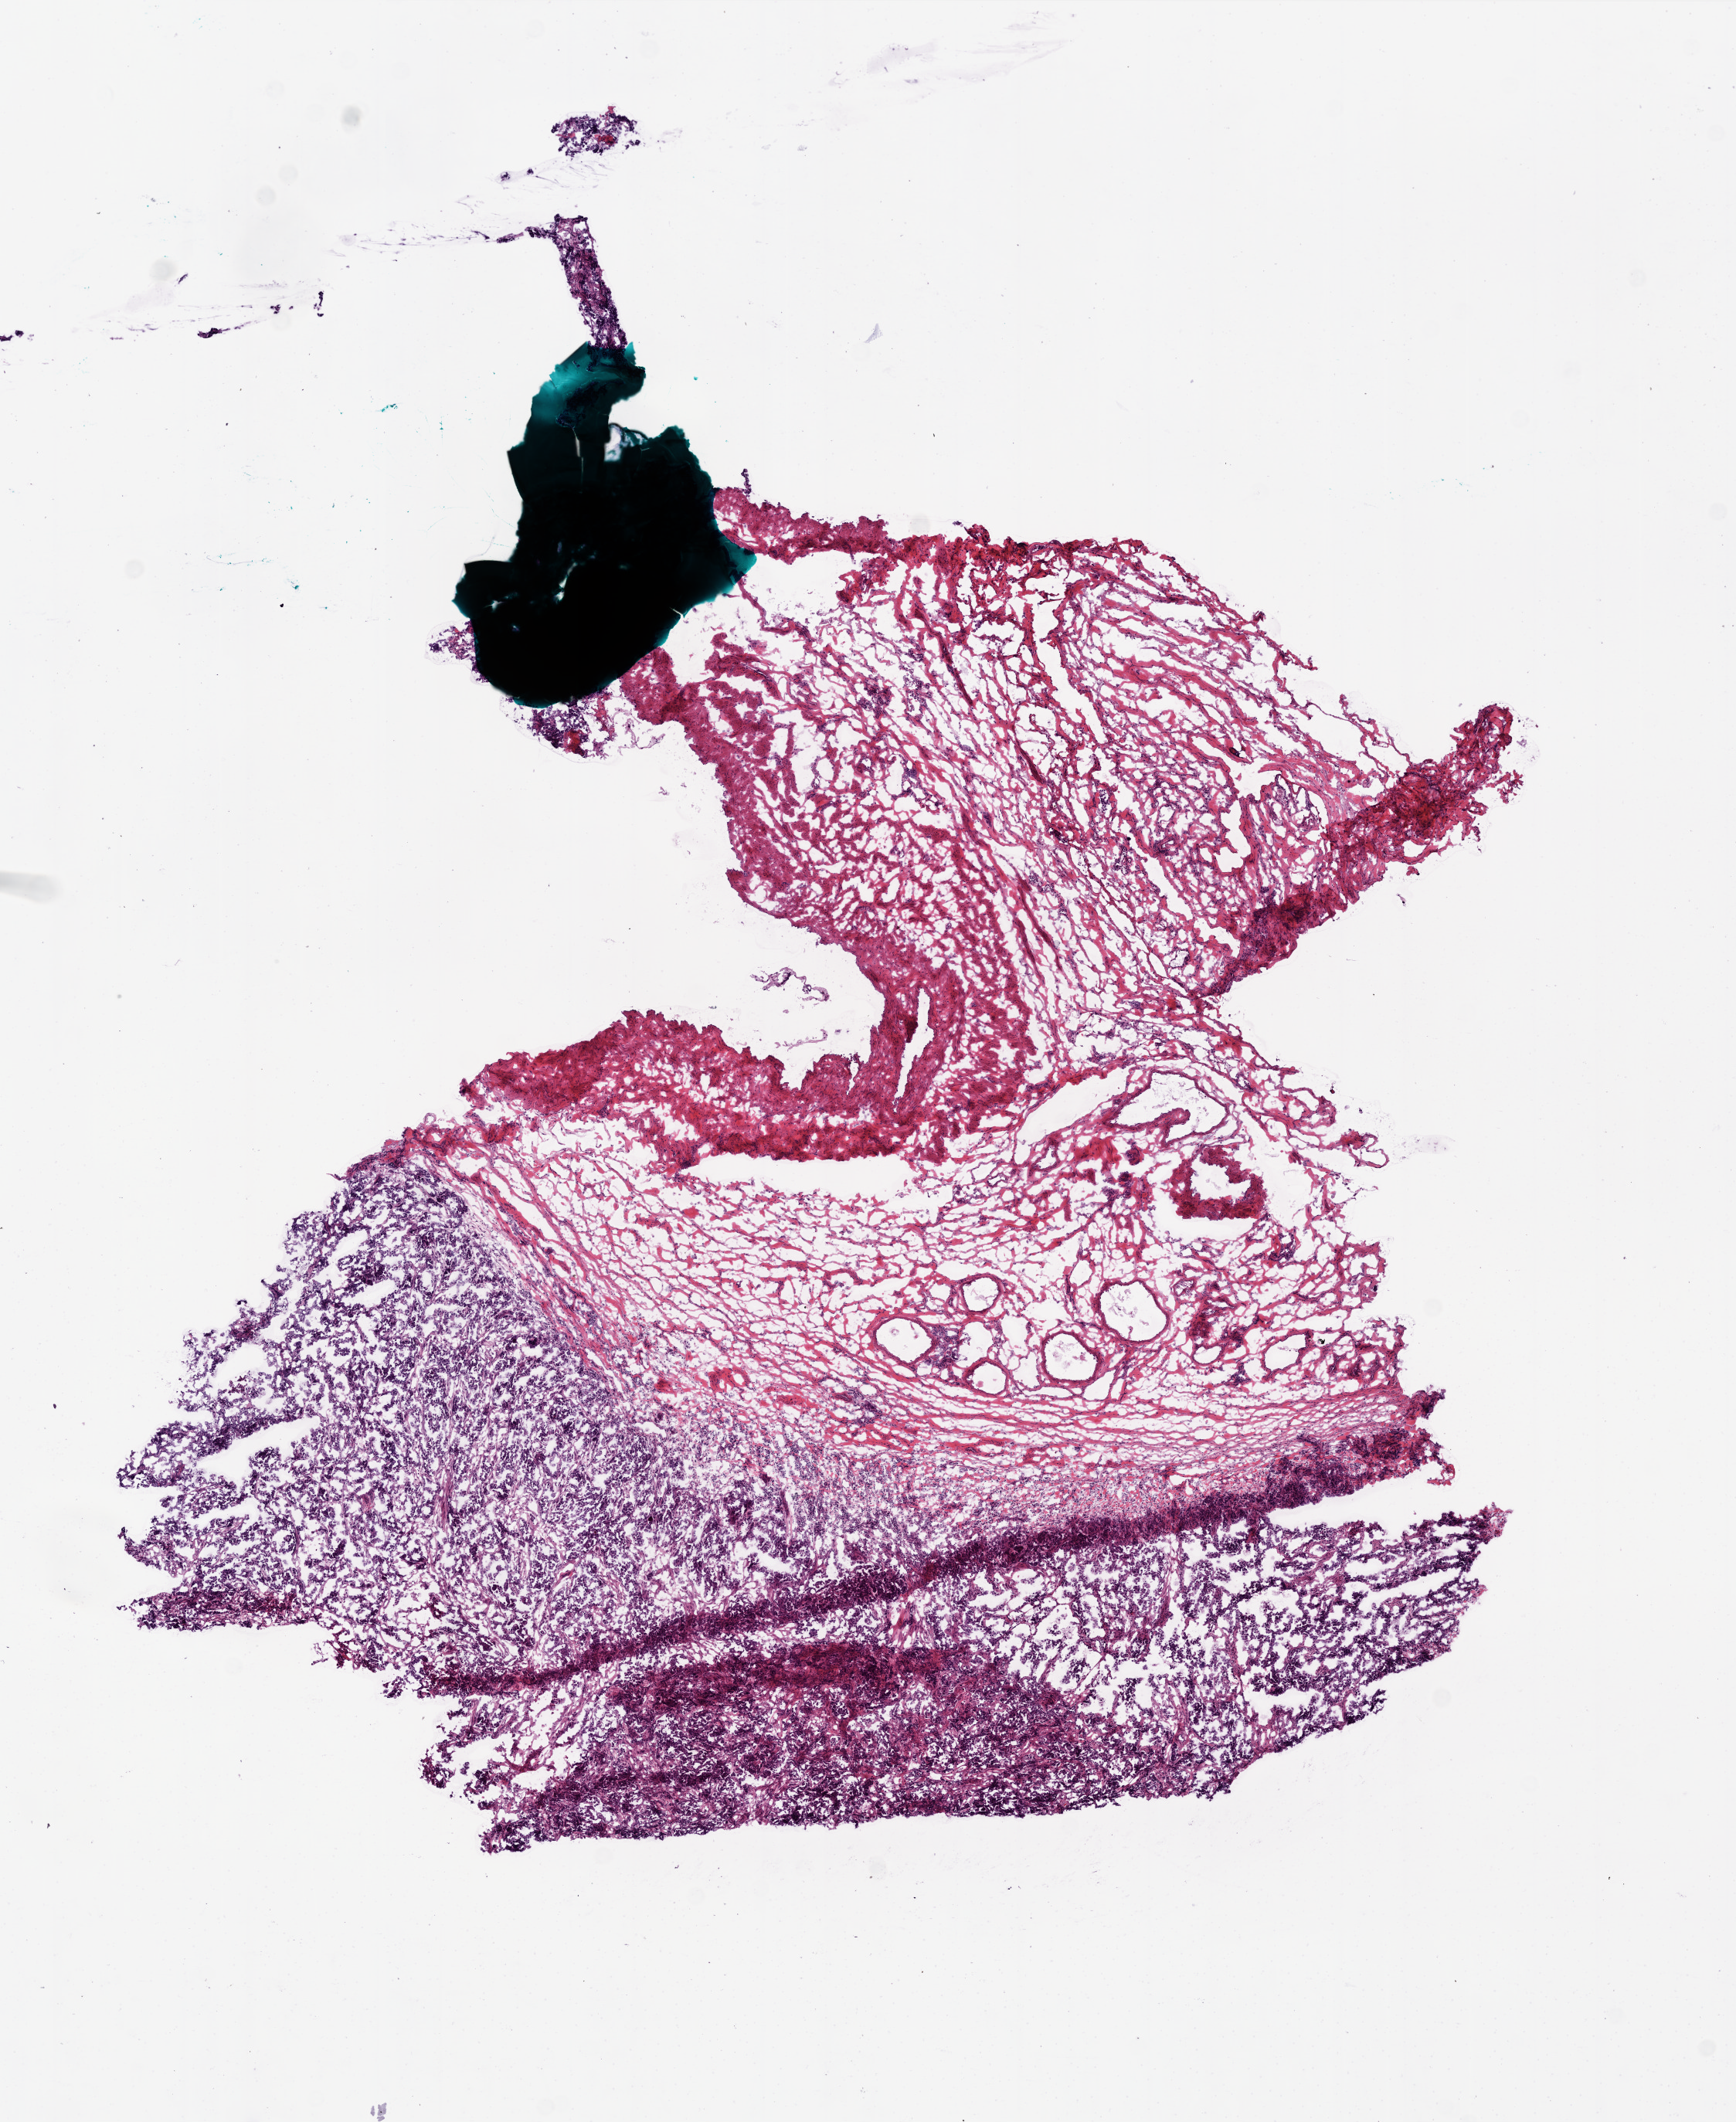
H&E whole-slide image, a low-resolution overview of the entire scanned area, about 9.0 x 11.0 mm, frozen section, primary tumour sample from the ovary. Patient: female, age at initial diagnosis 42 years. Histologic grade: G3 (poorly differentiated). Pathologist review of this section (percent, as recorded): tumour nuclei 70%, normal cells 0%, necrosis 5%.
Laterality: left. Histologic diagnosis: Serous cystadenocarcinoma, NOS. FIGO stage: IIIC.